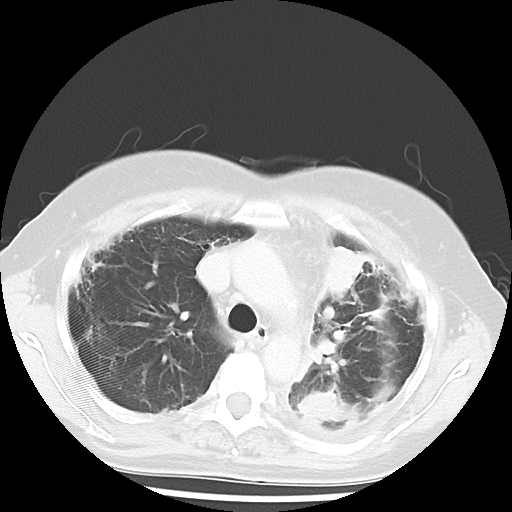
Chest CT, one axial slice; slice 40 of 56 in the series (ordered by position); reconstruction kernel LUNG; lung window (W 1500 / L -600 HU); 5 mm slice thickness; 512 × 512 image matrix. Patient: female, 56 years. From the clinical record (not read from this slice): clinical TNM (as recorded): T1c N0 M1.
Annotated regions visible in this slice (bounding box drawn by a radiologist):
- lung tumour (recorded histology: adenocarcinoma): box from (x=316, y=238) to (x=366, y=299) px